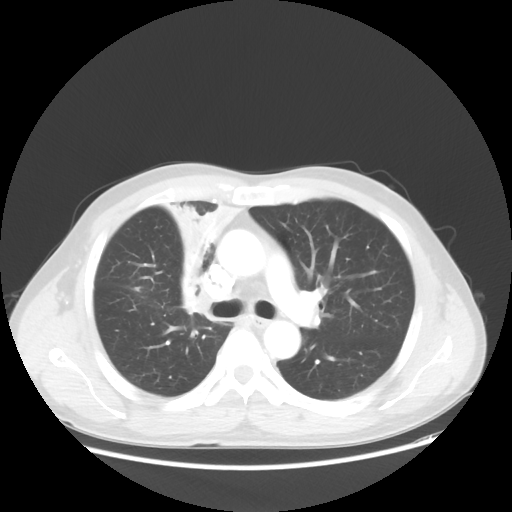
Chest CT, one axial slice. Slice 34 of 56 in the series (ordered by position). Reconstruction kernel STANDARD. 100 kVp. Lung window (W 1500 / L -600 HU). 5 mm slice thickness. 512 × 512 image matrix, field of view 398 × 398 mm. Male patient, age 60 years. From the clinical record (not read from this slice): clinical TNM (as recorded): T2a N1 M0.
Outlined on this slice (bounding box drawn by a radiologist):
- lung tumour (recorded histology: squamous cell carcinoma): bounding box (x1, y1, x2, y2) in pixels: (160, 190, 228, 312)